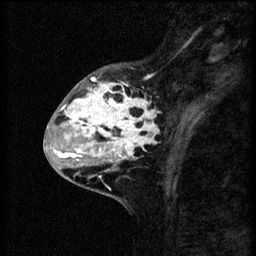
Breast MRI (dynamic contrast-enhanced), one sagittal slice. Slice 21 of 60 in the series (ordered by position). 3 images stored at this slice position (order not interpretable as contrast timing). 1.5 T. TE 4.2 ms, TR 8.2 ms. 2 mm slice thickness. 256 × 256 image matrix. Patient: female, 41 years.
Structures marked on this image (semi-automatic segmentation, software-assisted and operator-edited):
- analysis volume of interest (the breast-tissue region the enhancement analysis was run in; not a lesion): bounding box [x1, y1, x2, y2] px = [53, 64, 160, 175]
- tumour enhancement mask (voxels above the 70 % enhancement threshold inside the analysis volume of interest): [60, 76, 160, 157]